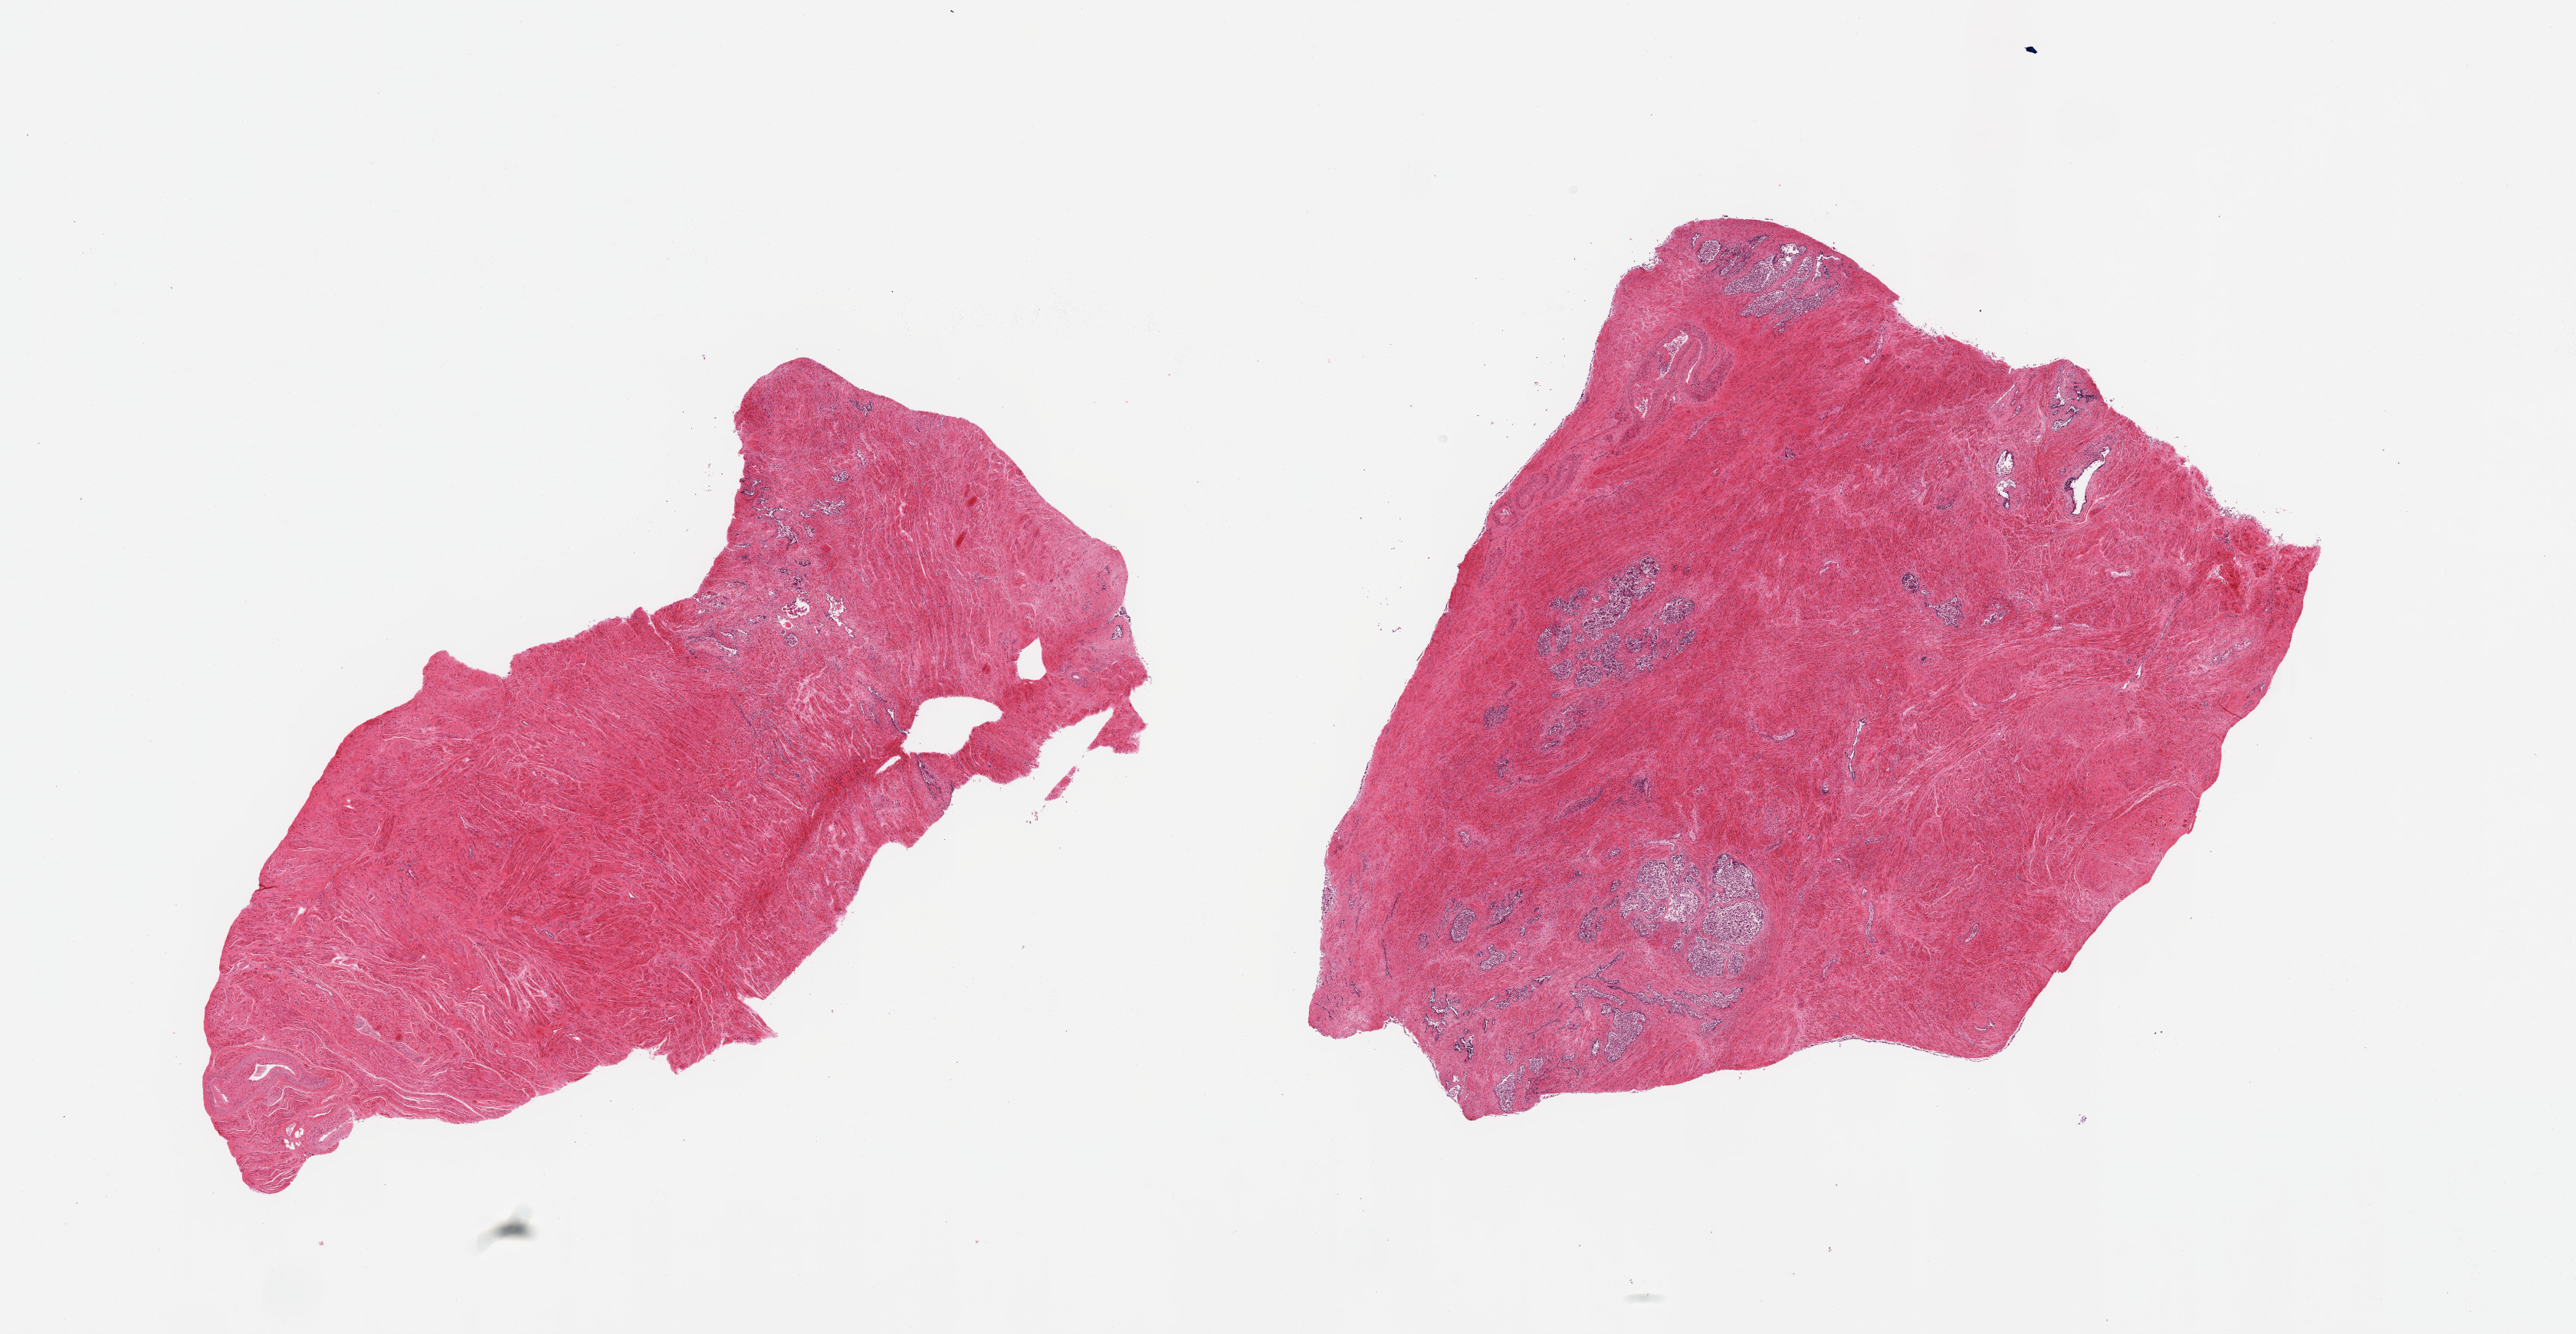
Whole-slide image, haematoxylin and eosin stain — whole scanned area (about 26.6 x 13.8 mm) shown as a low-resolution overview, PAXgene-fixed, paraffin-embedded tissue, target tissue: prostate, tissue donor sample.
Review note (as recorded): 2 pieces; glands totally autolyzed, stroma intact; stroma predominates.